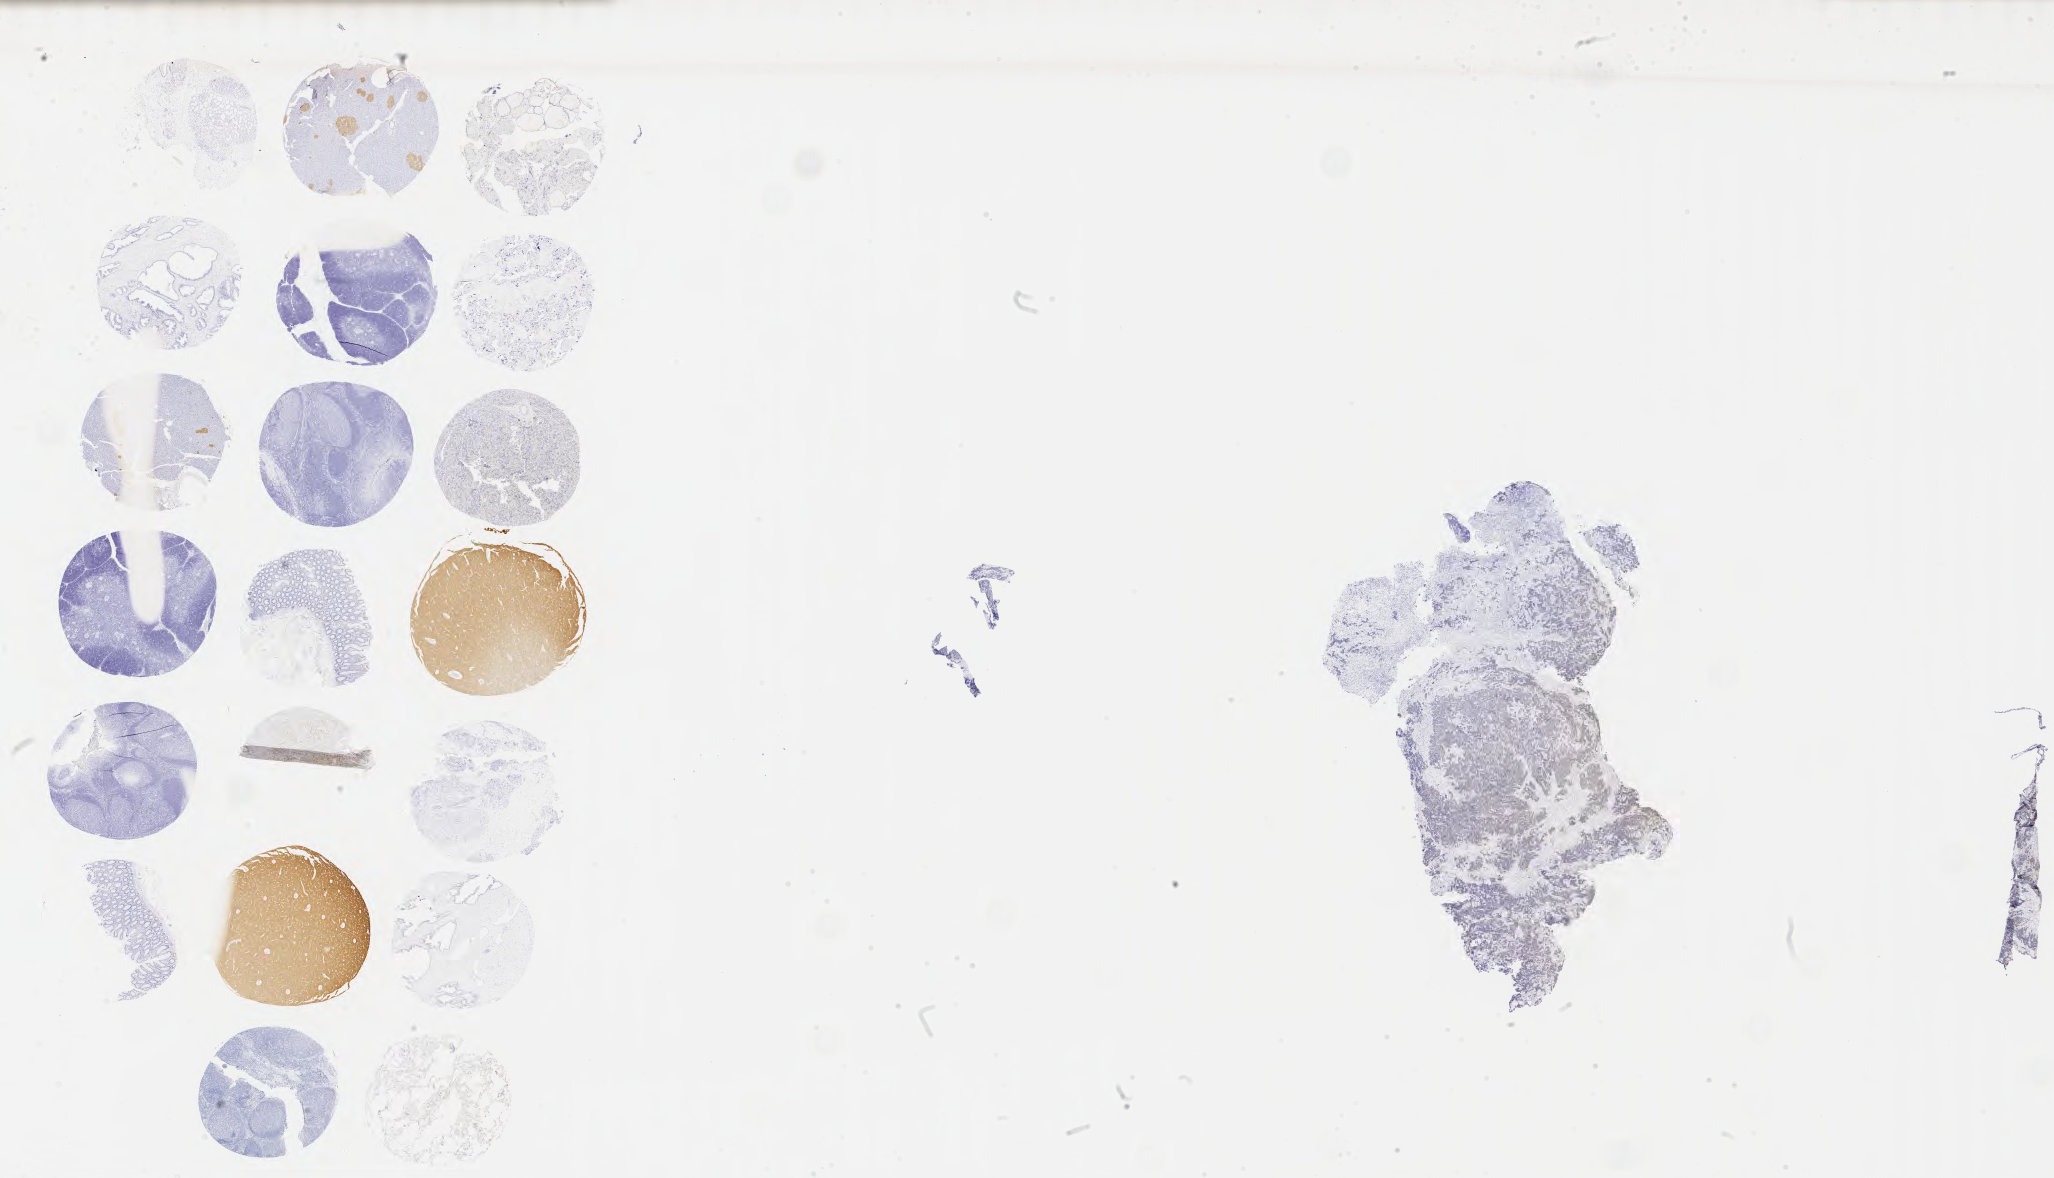
Immunohistochemistry (IHC) whole-slide image stained for synaptophysin, shown as a low-resolution overview of the whole scanned area (about 33.2 x 19.0 mm); tumor tissue; anatomic site: cervix. Patient female; age 43 years.
* diagnosis: Lymphoepithelial carcinoma